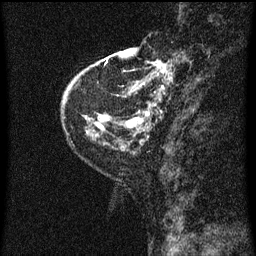
Breast MRI (dynamic contrast-enhanced), one sagittal slice; position 13 of 60 along the scan axis; dynamic contrast-enhanced series, image 2 of 3 at this slice position (ordered by acquisition); 1.5 T; TE 4.2 ms, TR 8 ms; 2 mm slice thickness; 256 × 256 image matrix. Patient: female, 48 years.
Annotated regions visible in this slice (semi-automatically segmented with operator editing):
- analysis volume of interest (the breast-tissue region the enhancement analysis was run in; not a lesion): bounding box <128,54,172,125> (left, top, right, bottom; pixels)
- tumour enhancement mask (voxels above the 70 % enhancement threshold inside the analysis volume of interest): <128,62,172,121>